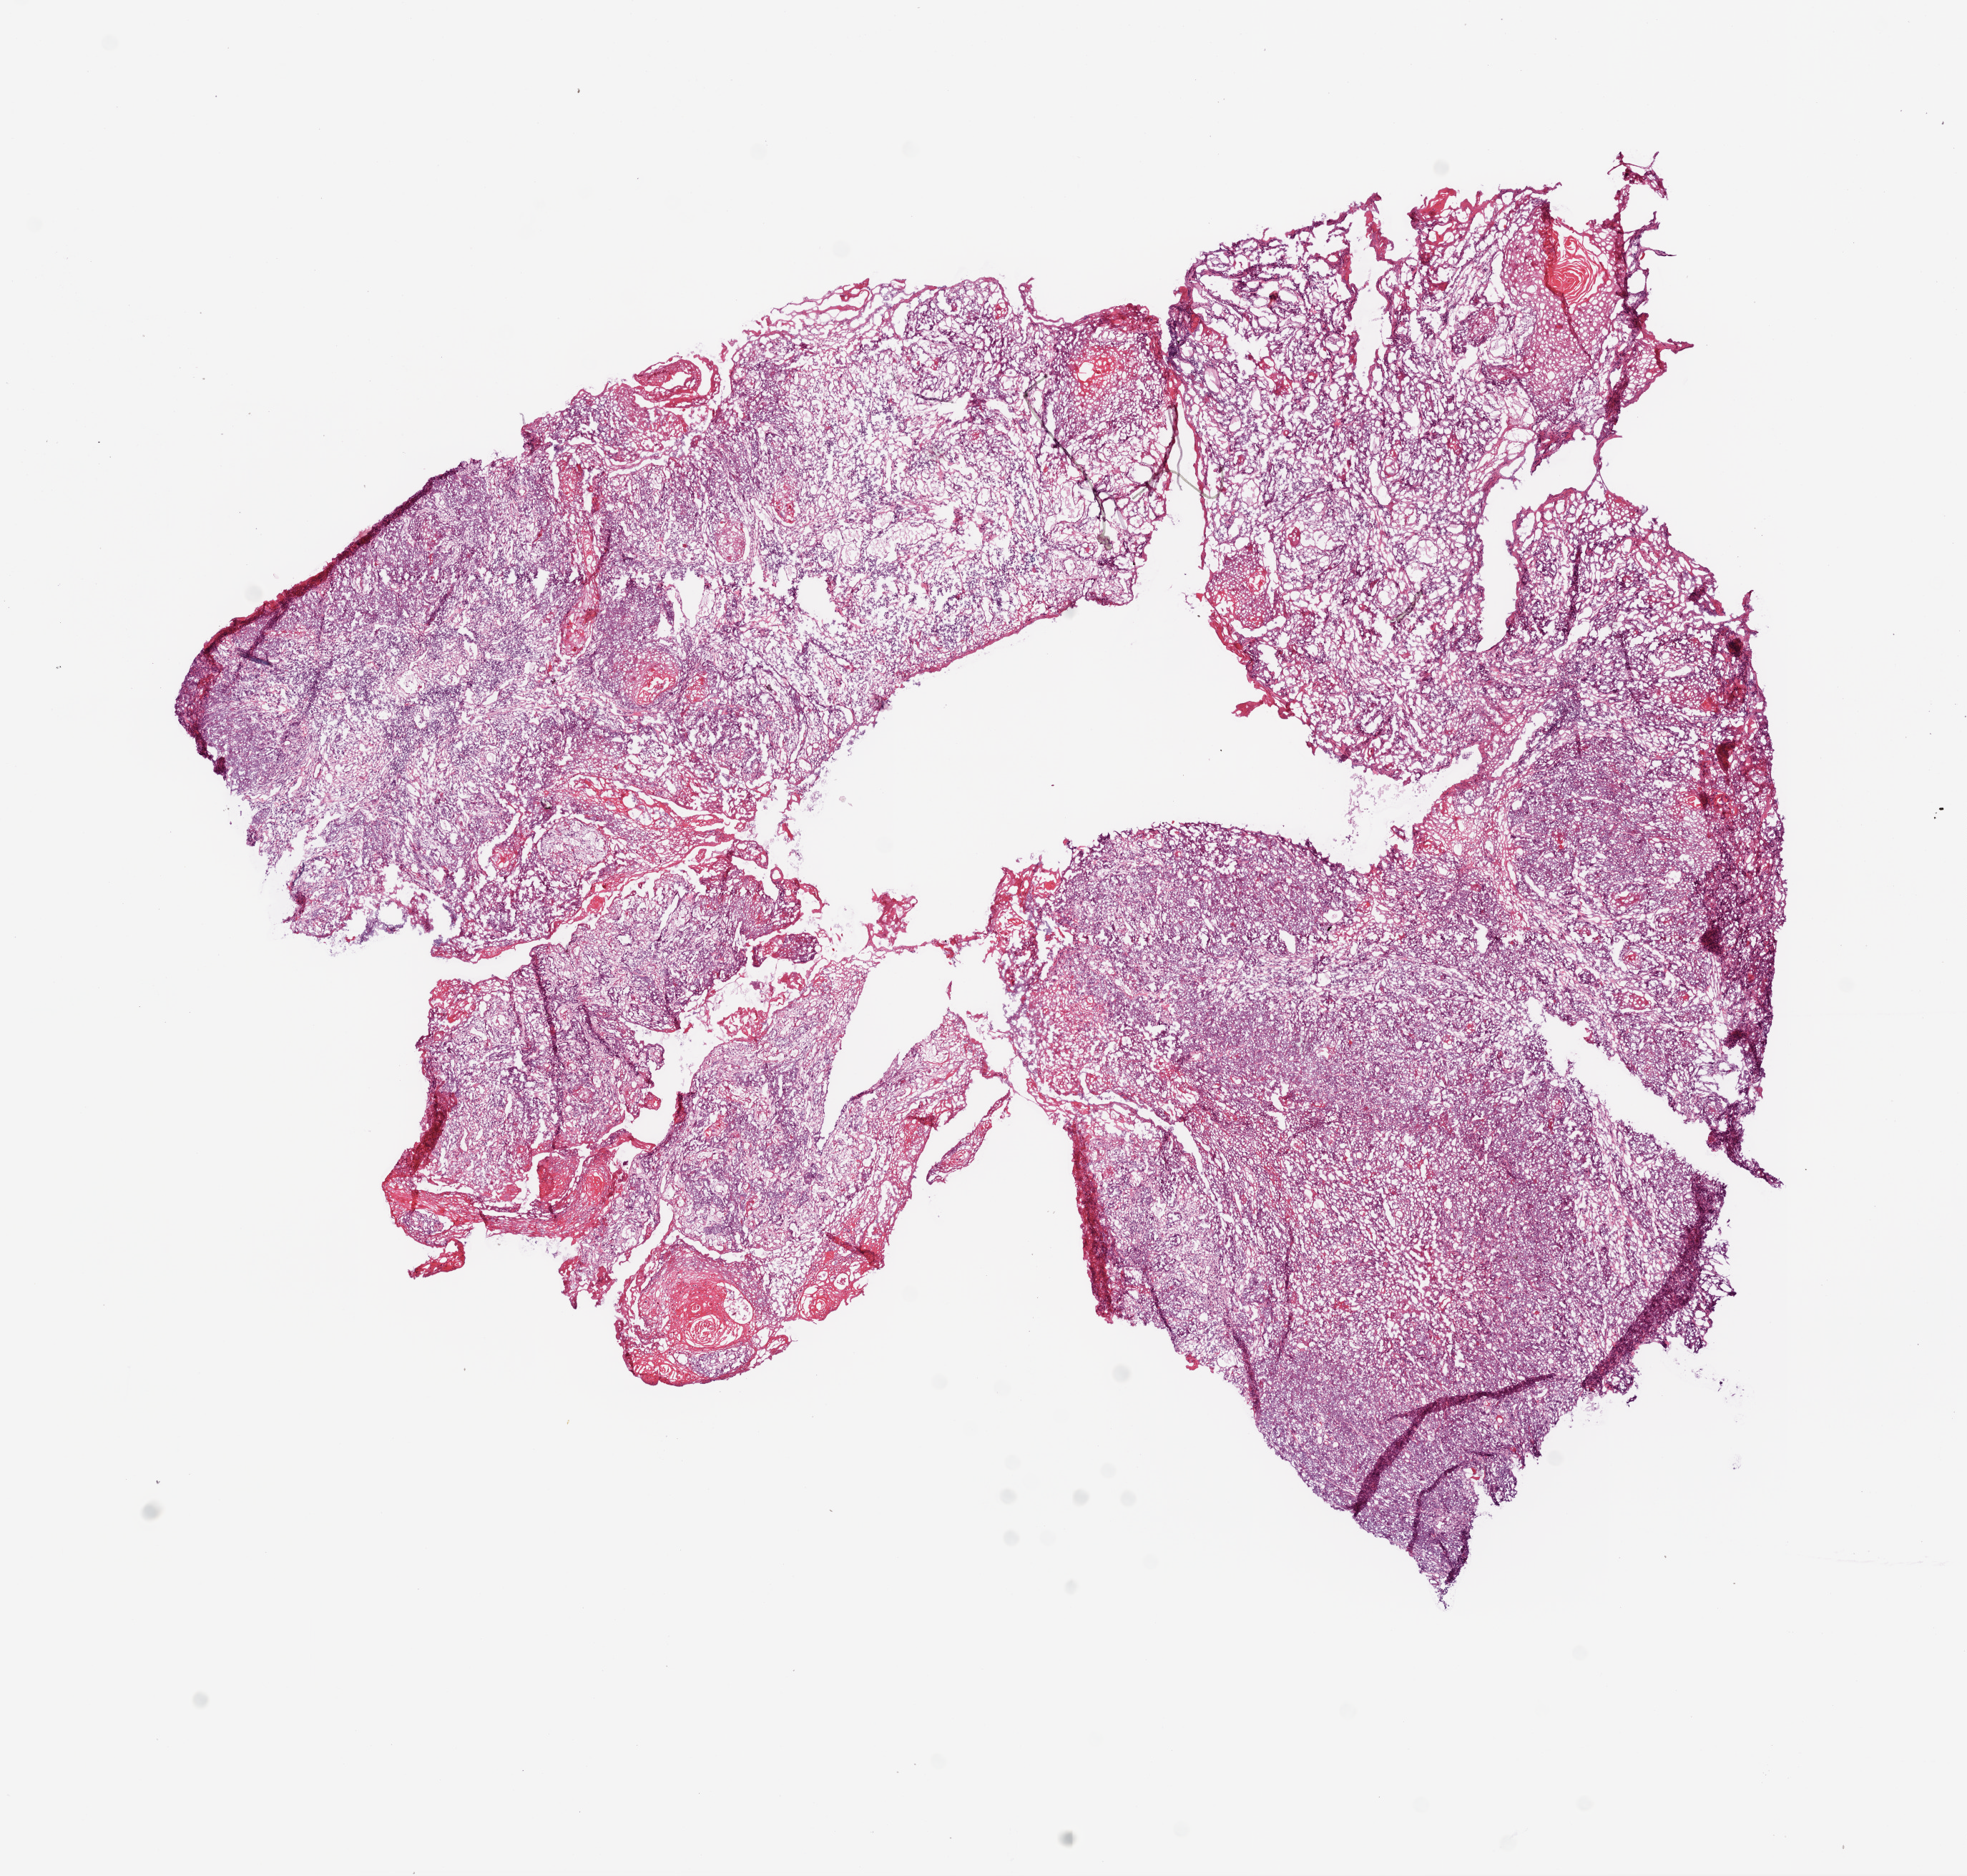
Digitized Hematoxylin and eosin (H&E) stained tissue section (whole slide) — low-resolution overview of the scanned area, about 11.0 x 10.5 mm (acquisition: 20x scan). Frozen section from the bottom of the tissue portion. Sample: primary tumour, head and neck. Male, age 47 years at initial diagnosis. Histologic grade: G2 (moderately differentiated). Composition of this section per pathologist review: tumour cells 80%, tumour nuclei 65%, normal cells 0%, stromal cells 20%, necrosis 0%.
Laterality: left. AJCC pathologic stage: IVA. Diagnosis: Squamous cell carcinoma, NOS (floor of mouth, NOS).